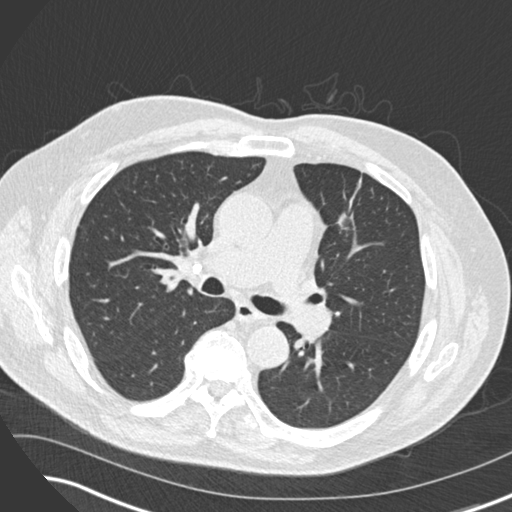
Low-dose screening chest CT, axial slice, third screening round (two years after baseline), lung window (W 1500 / L -600 HU), 2 mm slice thickness, 120 kVp, slice 72 of 169 in the series, 512 × 512 image matrix, field of view 360 × 360 mm. Male, age 74 years at enrolment. Former smoker at enrolment.
- Lesion marked by an expert reader, bounding box <318,196,375,247> (left, top, right, bottom; pixels).
- Screening reader's record for this exam (one nodule recorded; not confirmed to be the boxed lesion): non-calcified nodule or mass ≥4 mm, left upper lobe, 12 × 10 mm, spiculated (stellate) margins, soft tissue attenuation, pre-existing on the prior screen: yes; interval growth: yes.
- Official screen result: positive, other.
- Later outcome: lung cancer diagnosed 349 days after this screen — adenocarcinoma, NOS, left upper lobe, poorly differentiated (G3), stage IIIA (AJCC 6th edition), 27 mm at pathology.